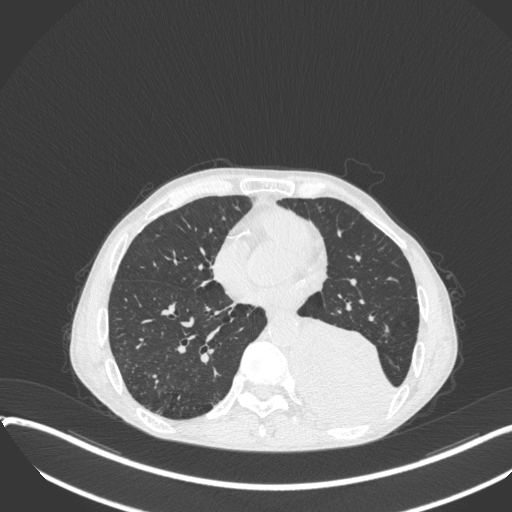
Chest CT, one axial slice. Position 141 of 400 along the scan axis. Reconstruction kernel B31f. 120 kVp. Lung window (W 1500 / L -600 HU). 1 mm slice thickness. 512 × 512 image matrix, field of view 400 × 400 mm. Male patient, age 57 years. Case-level facts recorded for this patient, not image findings: clinical TNM (as recorded): T4 N0 M0.
Annotated regions visible in this slice (bounding box drawn by a radiologist):
- lung tumour (recorded histology: squamous cell carcinoma): bounding box <295,310,398,429> (left, top, right, bottom; pixels)